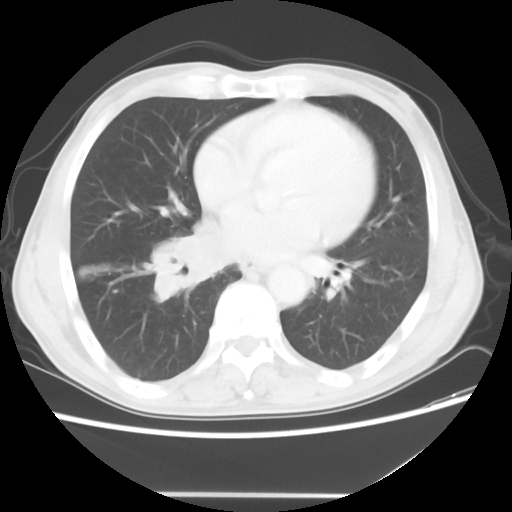
Chest CT, one axial slice. Slice 23 of 56 in the series (ordered by position). Lung window (W 1500 / L -600 HU). 5 mm slice thickness. 512 × 512 image matrix, field of view 344 × 344 mm. Male patient, age 65 years. From the clinical record (not read from this slice): clinical TNM (as recorded): T1c N3 M0; histopathological grade: G3.
Structures marked on this image (rectangle marked by the reading radiologist):
- lung tumour (recorded histology: small cell carcinoma): bounding box [x1, y1, x2, y2] px = [145, 211, 236, 306]